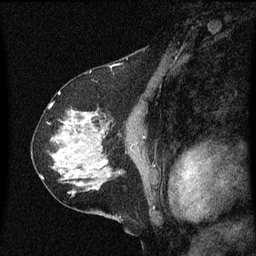
Breast MRI (dynamic contrast-enhanced), one sagittal slice. Slice 37 of 60 in the series (ordered by position). Dynamic contrast-enhanced series, image 2 of 3 at this slice position (ordered by acquisition). 1.5 T. TE 4.2 ms, TR 8 ms. 2 mm slice thickness. 256 × 256 image matrix, field of view 200 × 200 mm. Female patient, age 58 years.
Outlined on this slice (semi-automatic segmentation, software-assisted and operator-edited):
- analysis volume of interest (the breast-tissue region the enhancement analysis was run in; not a lesion): bounding box <56,112,99,149> (left, top, right, bottom; pixels)
- tumour enhancement mask (voxels above the 70 % enhancement threshold inside the analysis volume of interest): <67,114,87,125>